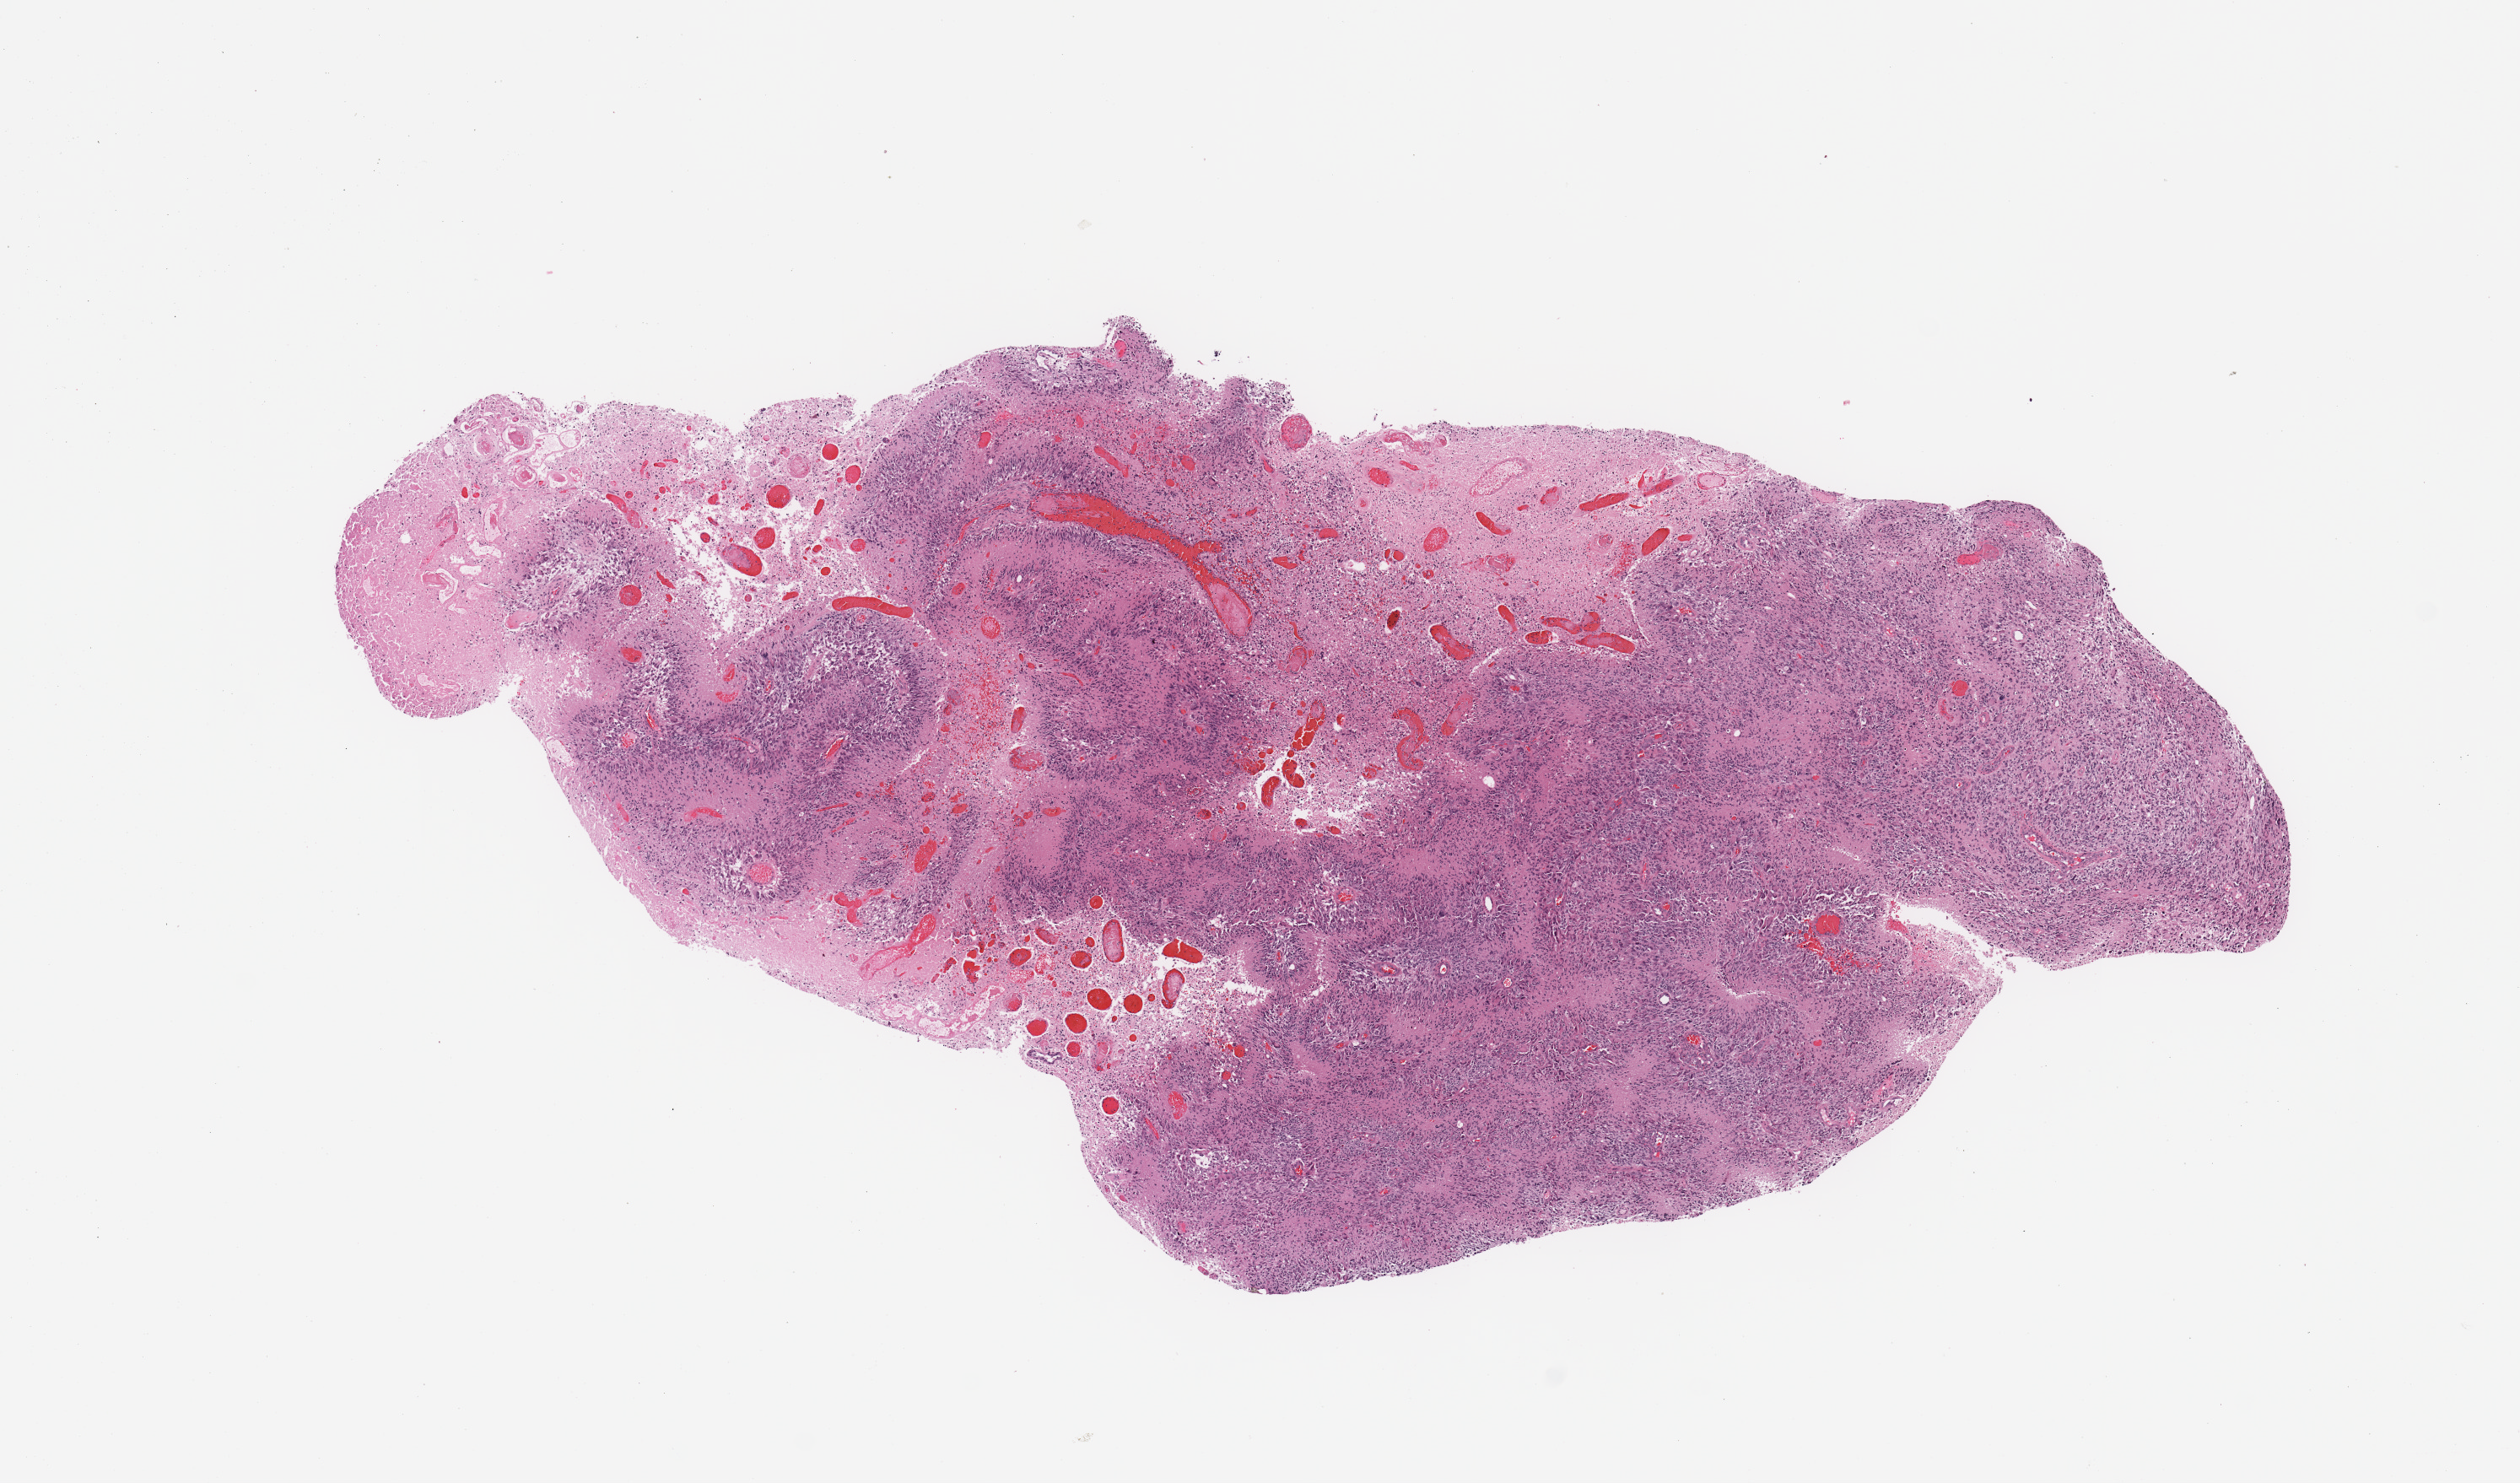
H&E whole-slide image — shown as a low-resolution overview of the whole scanned area (about 11.8 x 7.0 mm, acquisition: 20x scan). Tumour tissue sample, brain. Female, 51 y/o.
- primary tumour site (as recorded): parietal lobe
- diagnosis: Glioblastoma